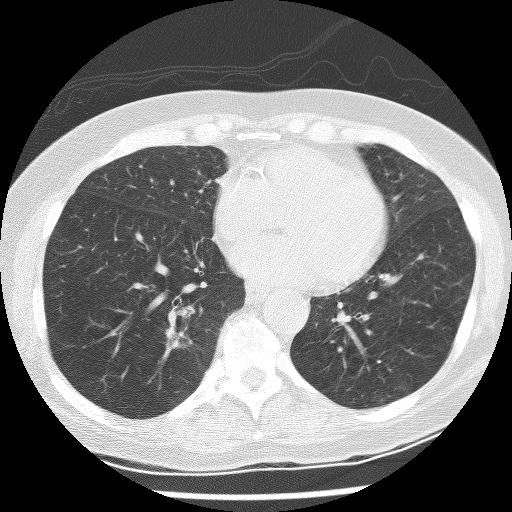
Low-dose screening chest CT, one axial slice; position 98 of 247 along the scan axis; reconstruction kernel BONE; 120 kVp; lung window (W 1500 / L -600 HU); 2.5 mm slice thickness; 512 × 512 image matrix, field of view 300 × 300 mm.
Outlined on this slice (manually delineated by an expert):
- lesion 1 (tumor, lower lobe of right lung): bounding box [x1, y1, x2, y2] px = [162, 327, 192, 360]